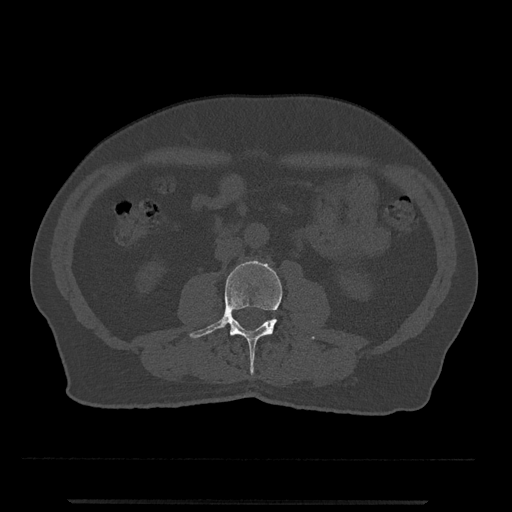
CT including the spine, one axial slice; slice 199 of 797 in the series (ordered by position); reconstruction kernel Br40s/3; bone window (W 1800 / L 400 HU); 0.5 mm slice thickness; 512 × 512 image matrix, field of view 419 × 419 mm. Patient: male, 63 years. From the clinical record (not read from this slice): primary cancer: prostate.
Outlined on this slice (semi-automatically segmented with operator editing):
- L3 vertebra: bounding box <189,260,315,374> (left, top, right, bottom; pixels)